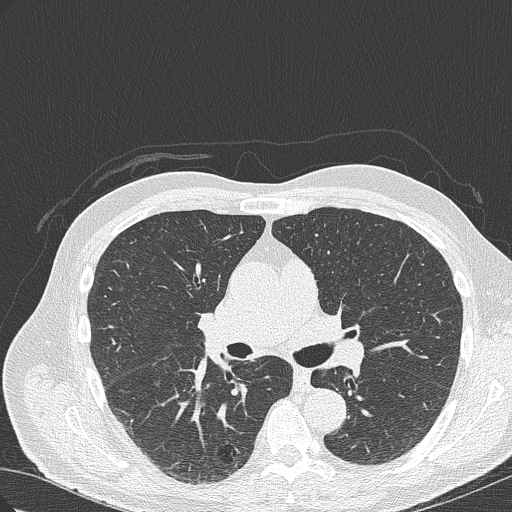
Chest CT (low-dose screening protocol), one axial image; baseline screening round; lung window (W 1500 / L -600 HU); 1 mm slice thickness; slice 133 of 322 in the series; 512 × 512 image matrix. Male participant, aged 70 years at enrolment. Current smoker at enrolment.
• Expert-annotated lung lesion, box from (x=199, y=419) to (x=262, y=474) px.
• The screening reader recorded 4 non-calcified nodules or masses ≥4 mm on this exam (right lower lobe, right lower lobe, right upper lobe, right lower lobe); which of them this box marks is not recorded.
• Official screen result: positive, change unspecified: nodule(s) >= 4 mm or enlarging nodule(s), mass(es), or other non-specific abnormalities suspicious for lung cancer.
• Later outcome: lung cancer diagnosed 978 days after this screen (after the third annual screen) — bronchiolo-alveolar adenocarcinoma, NOS, right lower lobe, poorly differentiated (G3), stage IB (AJCC 6th edition), 30 mm at pathology.